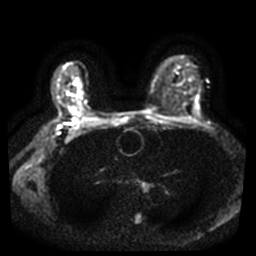
Breast MRI, one axial slice. Position 26 of 44 along the scan axis. Diffusion-weighted series; image 2 of 4 stored at this slice position (different b-values; order by instance number). 3 T. 5 mm slice thickness. 256 × 256 image matrix, field of view 340 × 340 mm. Female patient.
Annotated regions visible in this slice (manually delineated by an expert):
- tumour on diffusion-weighted imaging: bounding box (x1, y1, x2, y2) in pixels: (68, 107, 76, 114)